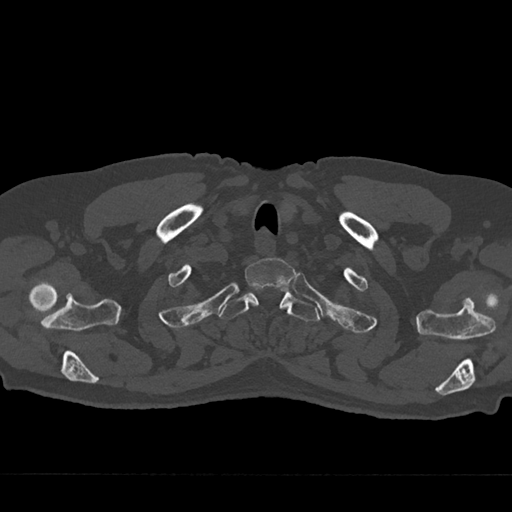
CT including the spine, one axial slice; 120 kVp; bone window (W 1800 / L 400 HU); 0.5 mm slice thickness; 512 × 512 image matrix, field of view 377 × 377 mm. Male patient, age 75 years. Case-level facts recorded for this patient, not image findings: primary cancer: renal.
Structures marked on this image (semi-automatically segmented with operator editing):
- T1 vertebra: box from (x=245, y=258) to (x=295, y=309) px
- T2 vertebra: (x=220, y=290)–(x=320, y=322)